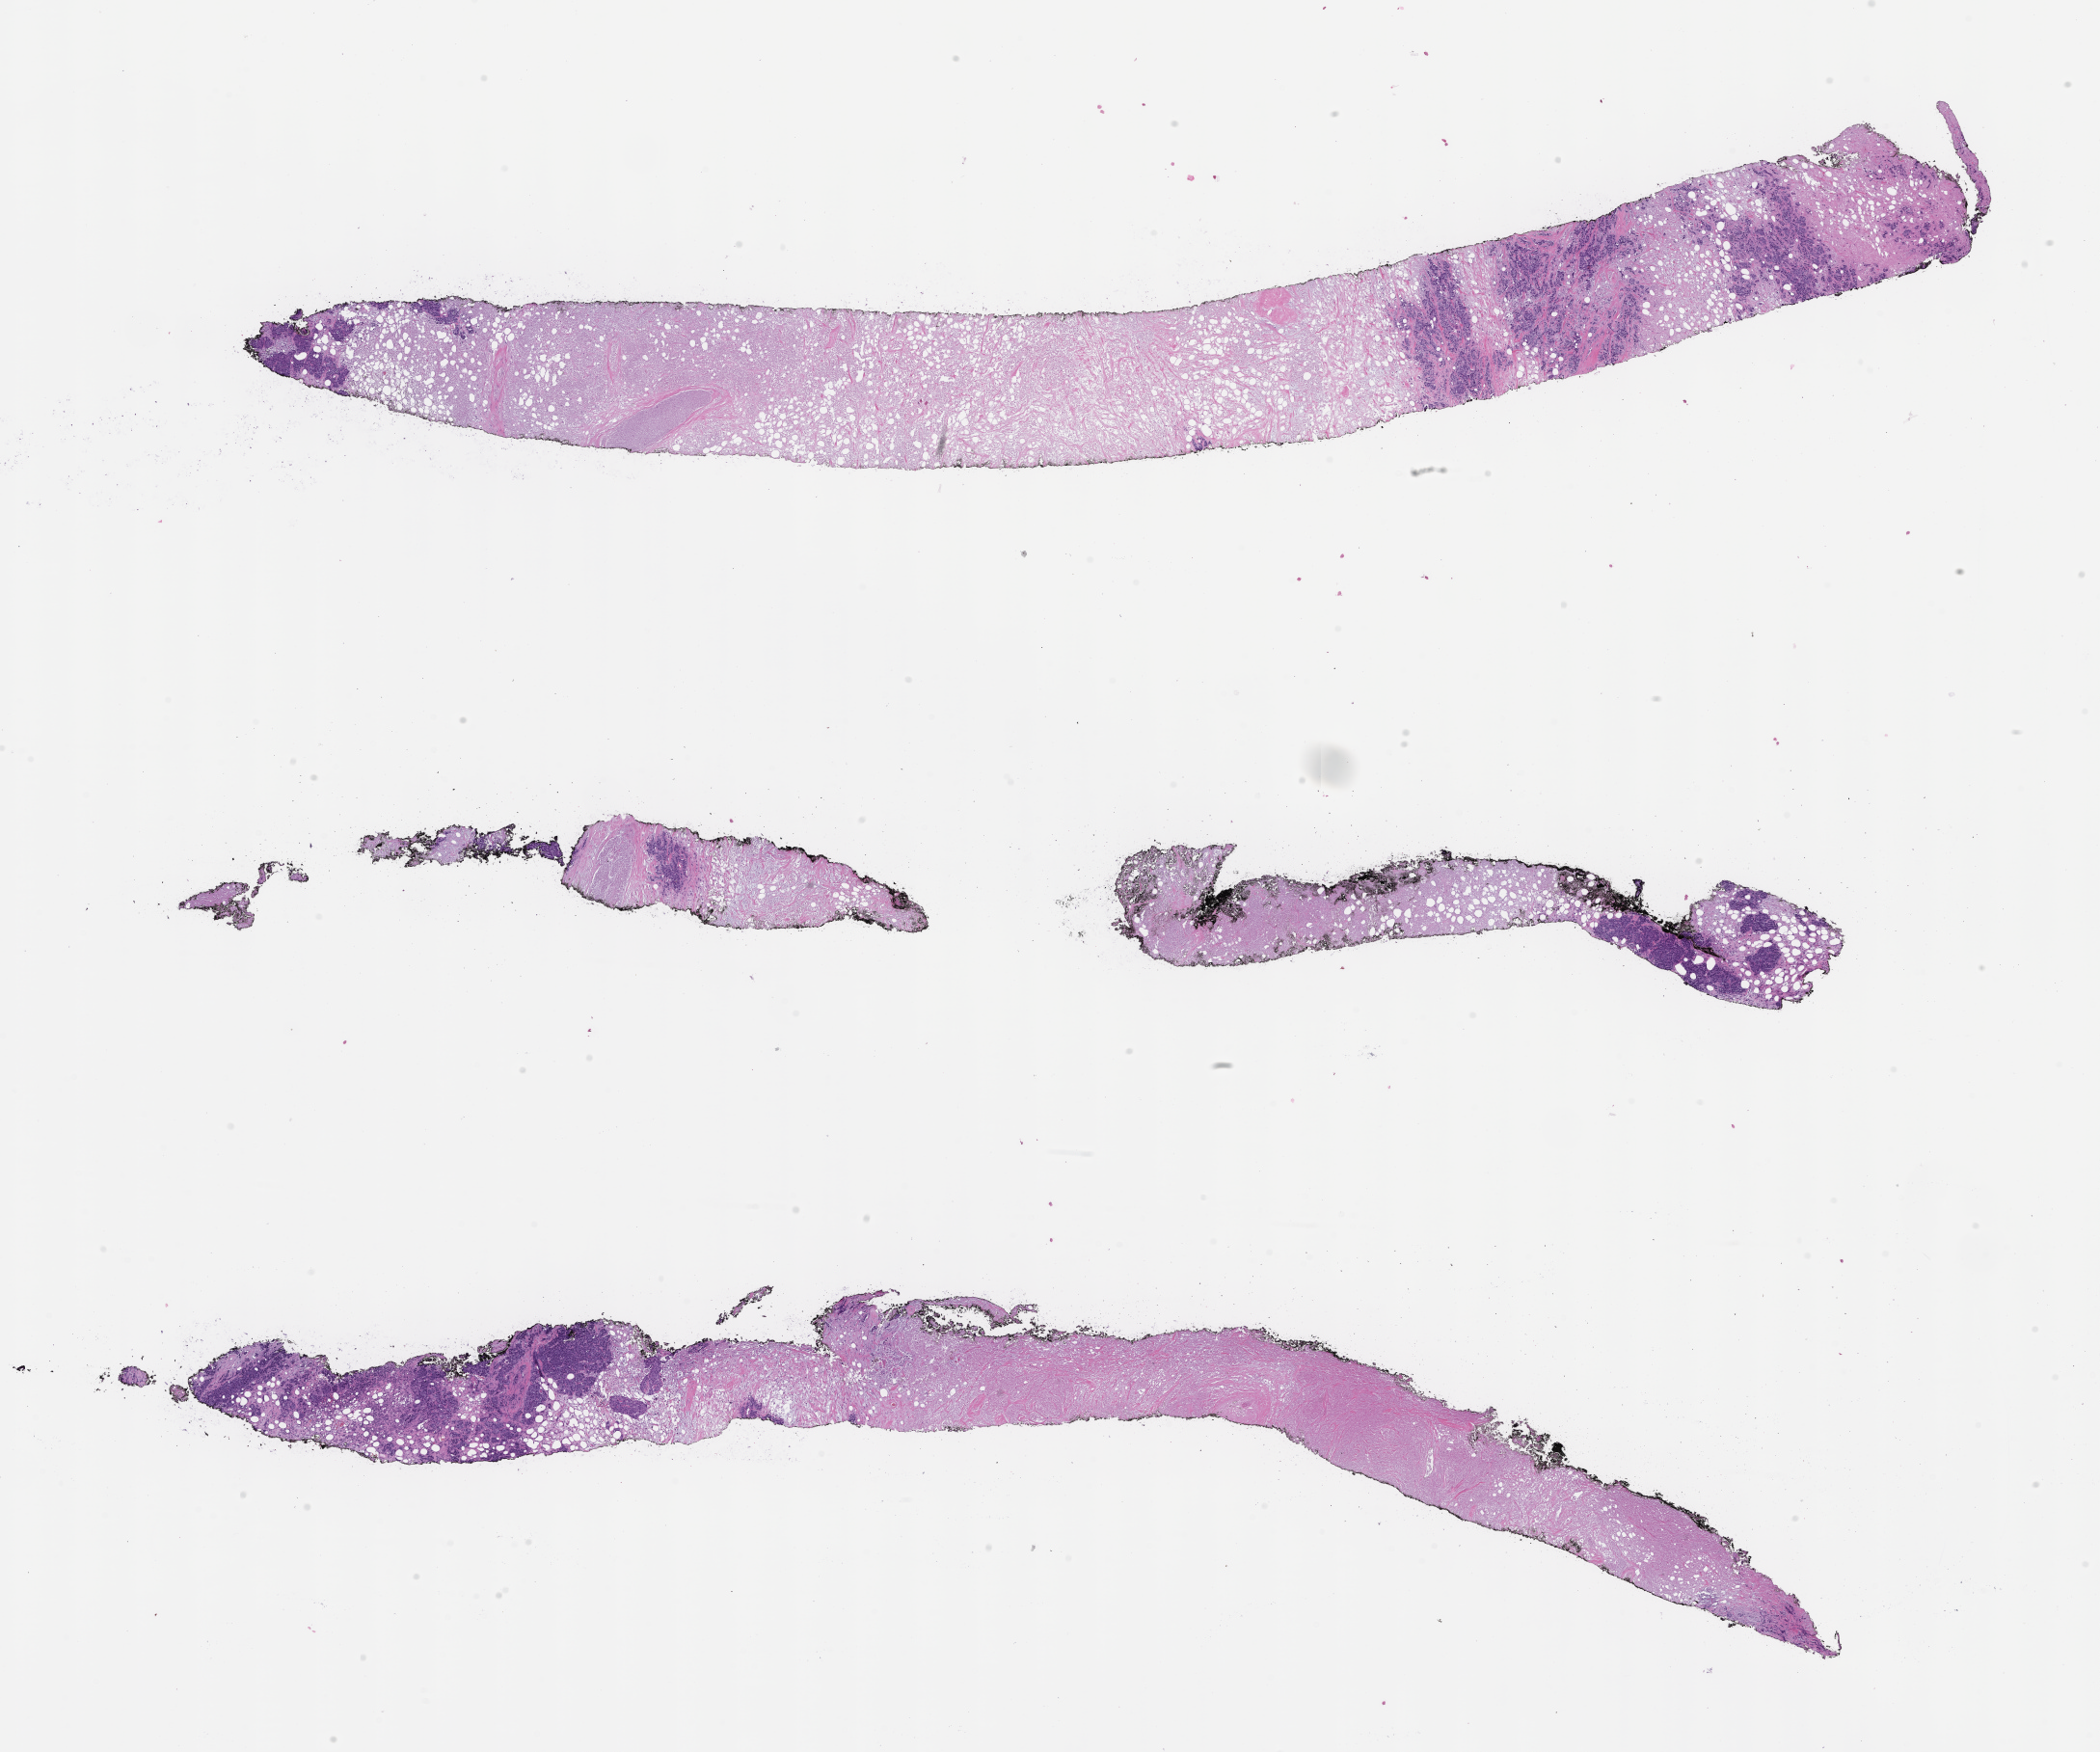
Whole-slide image, haematoxylin and eosin stain — a low-resolution overview of the entire scanned area, about 17.6 x 14.7 mm, FFPE section, tissue site: breast. Patient: female.
This section: primary tumour tissue. Diagnosis: Invasive Breast Carcinoma.